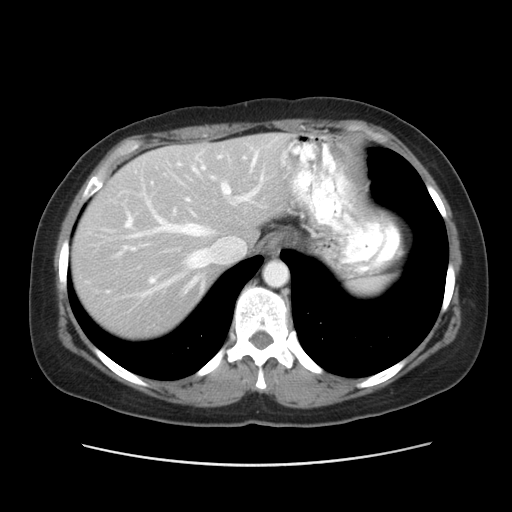
Contrast-enhanced abdominal CT, one axial slice; reconstruction kernel STANDARD; 120 kVp; intravenous contrast given; soft-tissue window (W 400 / L 40 HU); 5 mm slice thickness; 512 × 512 image matrix. Female patient, age 48 years. Case-level facts recorded for this patient, not image findings: diagnosis: colorectal cancer liver metastases, imaged before liver resection; multiple liver metastases: yes; largest metastasis: 4.5 cm; disease in both lobes: yes.
Structures marked on this image (outlined manually by an expert reader):
- hepatic veins: box from (x=123, y=151) to (x=265, y=296) px
- liver: (x=73, y=134)–(x=289, y=336)
- planned liver remnant (the part of the liver to remain after resection): (x=149, y=134)–(x=290, y=242)
- portal vein (with intrahepatic branches): (x=124, y=156)–(x=221, y=250)